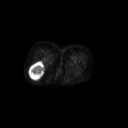
FDG PET of an extremity soft-tissue mass (from a PET/CT study), one axial slice. Slice 38 of 267 in the series (ordered by position). 3.27 mm slice thickness. 128 × 128 image matrix, field of view 700 × 700 mm. Patient: female, 70 years. From the clinical record (not read from this slice): histological type: synovial sarcoma; grade: intermediate; site of the primary tumour: right buttock.
Structures marked on this image (expert contour drawn on MRI and transferred to this co-registered scan by the dataset authors):
- gross tumour volume including surrounding oedema: box from (x=29, y=61) to (x=44, y=79) px
- gross tumour volume (mass): (x=29, y=62)–(x=44, y=79)